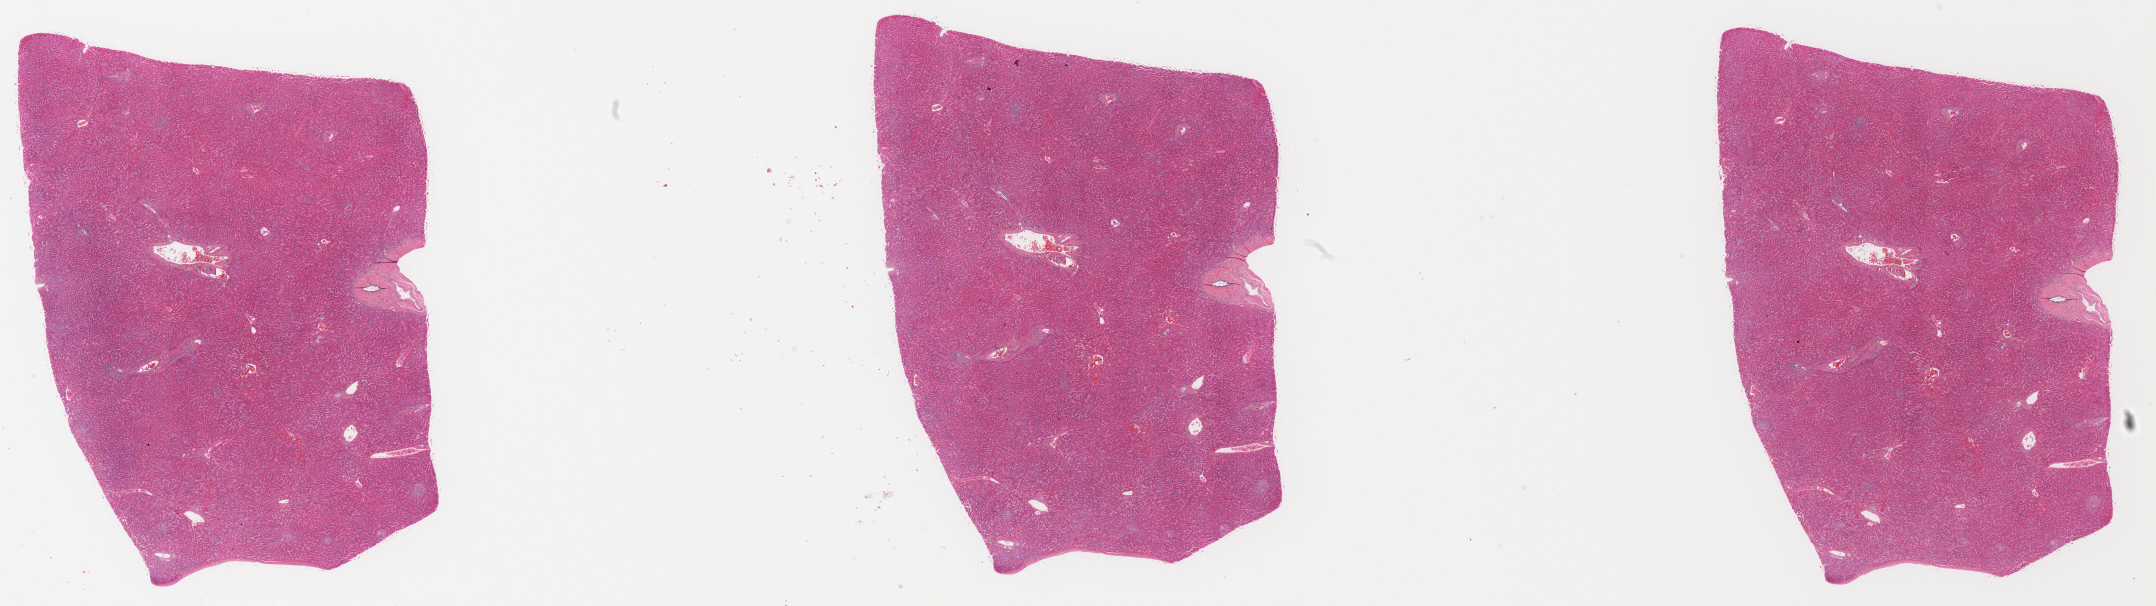
Whole-slide histology image, Hematoxylin and eosin (H&E) stained, low-resolution overview of the scanned area, about 34.1 x 9.6 mm (acquisition: 40x scan). Formalin-fixed paraffin-embedded (FFPE) diagnostic section. Primary tumour sample from the liver. Patient: female, age at initial diagnosis 62 years. Histologic grade: G2 (moderately differentiated).
Histologic diagnosis: Hepatocellular carcinoma, NOS. AJCC pathologic stage: IIIA (6th edition).